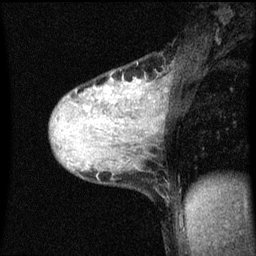
Breast MRI (dynamic contrast-enhanced), one sagittal slice; position 32 of 60 along the scan axis; dynamic contrast-enhanced series, image 2 of 3 at this slice position (ordered by acquisition); 1.5 T; TE 4.2 ms, TR 8.4 ms; 2 mm slice thickness; 256 × 256 image matrix. Patient: female, 36 years.
Outlined on this slice (semi-automatically segmented with operator editing):
- analysis volume of interest (the breast-tissue region the enhancement analysis was run in; not a lesion): bounding box [x1, y1, x2, y2] px = [52, 72, 161, 151]
- tumour enhancement mask (voxels above the 70 % enhancement threshold inside the analysis volume of interest): [108, 92, 111, 95]